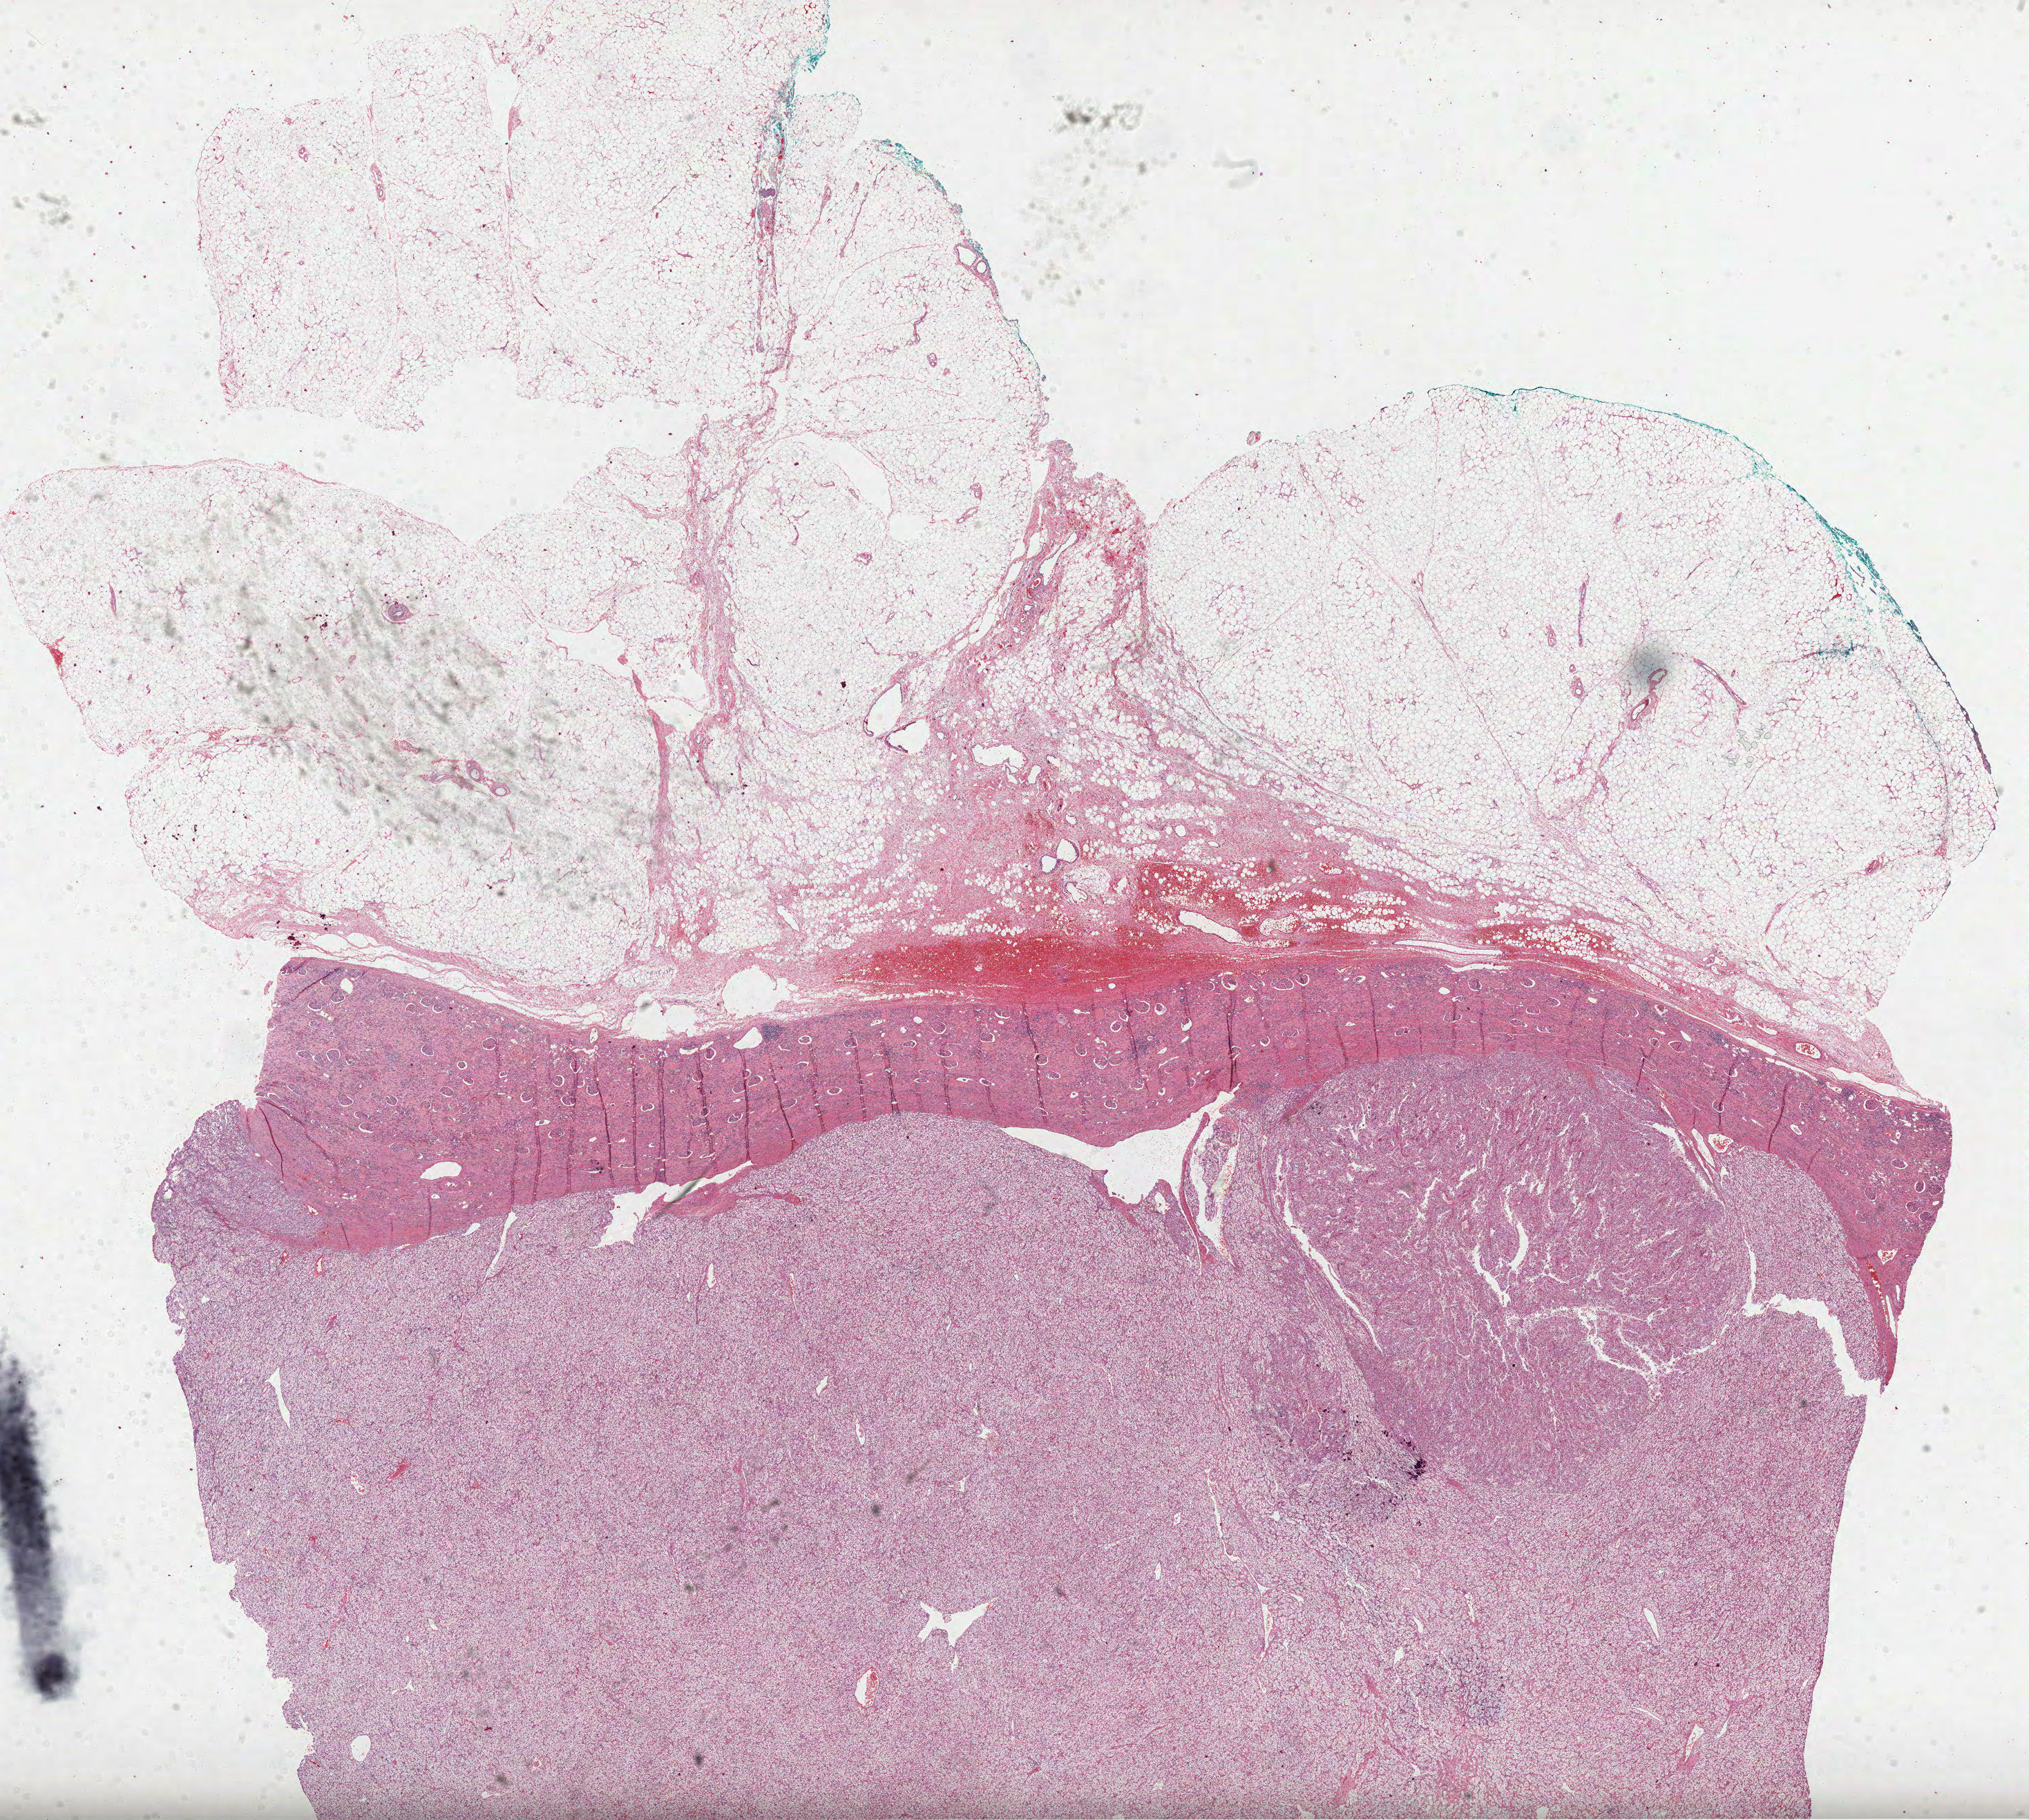
H&E-stained whole-slide image, a low-resolution overview of the entire scanned area, about 23.7 x 21.3 mm (acquisition: 40x scan). FFPE section. Primary tumour sample from the kidney. Male, age 71 years at initial diagnosis. Histologic grade: G3 (poorly differentiated).
Diagnosis: Clear cell adenocarcinoma, NOS. AJCC pathologic stage: III. TNM: T3a N0 M0. Laterality: left.